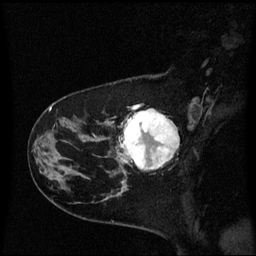
Breast MRI (dynamic contrast-enhanced), one sagittal slice. Dynamic contrast-enhanced series, image 2 of 3 at this slice position (ordered by acquisition). 1.5 T. TE 4.2 ms, TR 8.4 ms. 2 mm slice thickness. 256 × 256 image matrix, field of view 220 × 220 mm. Female patient, age 41 years. Case-level facts recorded for this patient, not image findings: setting: breast cancer imaged before/during neoadjuvant chemotherapy; receptor status: triple-negative.
Annotated regions visible in this slice (semi-automatic segmentation, software-assisted and operator-edited):
- analysis volume of interest (the breast-tissue region the enhancement analysis was run in; not a lesion): bounding box <116,108,179,177> (left, top, right, bottom; pixels)
- tumour enhancement mask (voxels above the 70 % enhancement threshold inside the analysis volume of interest): <121,110,179,171>